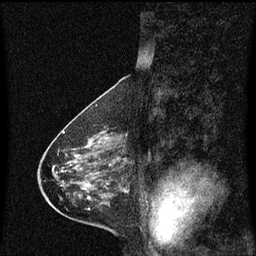
Breast MRI (dynamic contrast-enhanced), one sagittal slice. Position 30 of 60 along the scan axis. Dynamic contrast-enhanced series, image 2 of 3 at this slice position (ordered by acquisition). 1.5 T. TE 4.2 ms, TR 8.4 ms. 2 mm slice thickness. 256 × 256 image matrix. Patient: female, 58 years.
Outlined on this slice (semi-automatic segmentation, software-assisted and operator-edited):
- analysis volume of interest (the breast-tissue region the enhancement analysis was run in; not a lesion): bounding box <100,130,127,160> (left, top, right, bottom; pixels)
- tumour enhancement mask (voxels above the 70 % enhancement threshold inside the analysis volume of interest): <100,132,119,160>